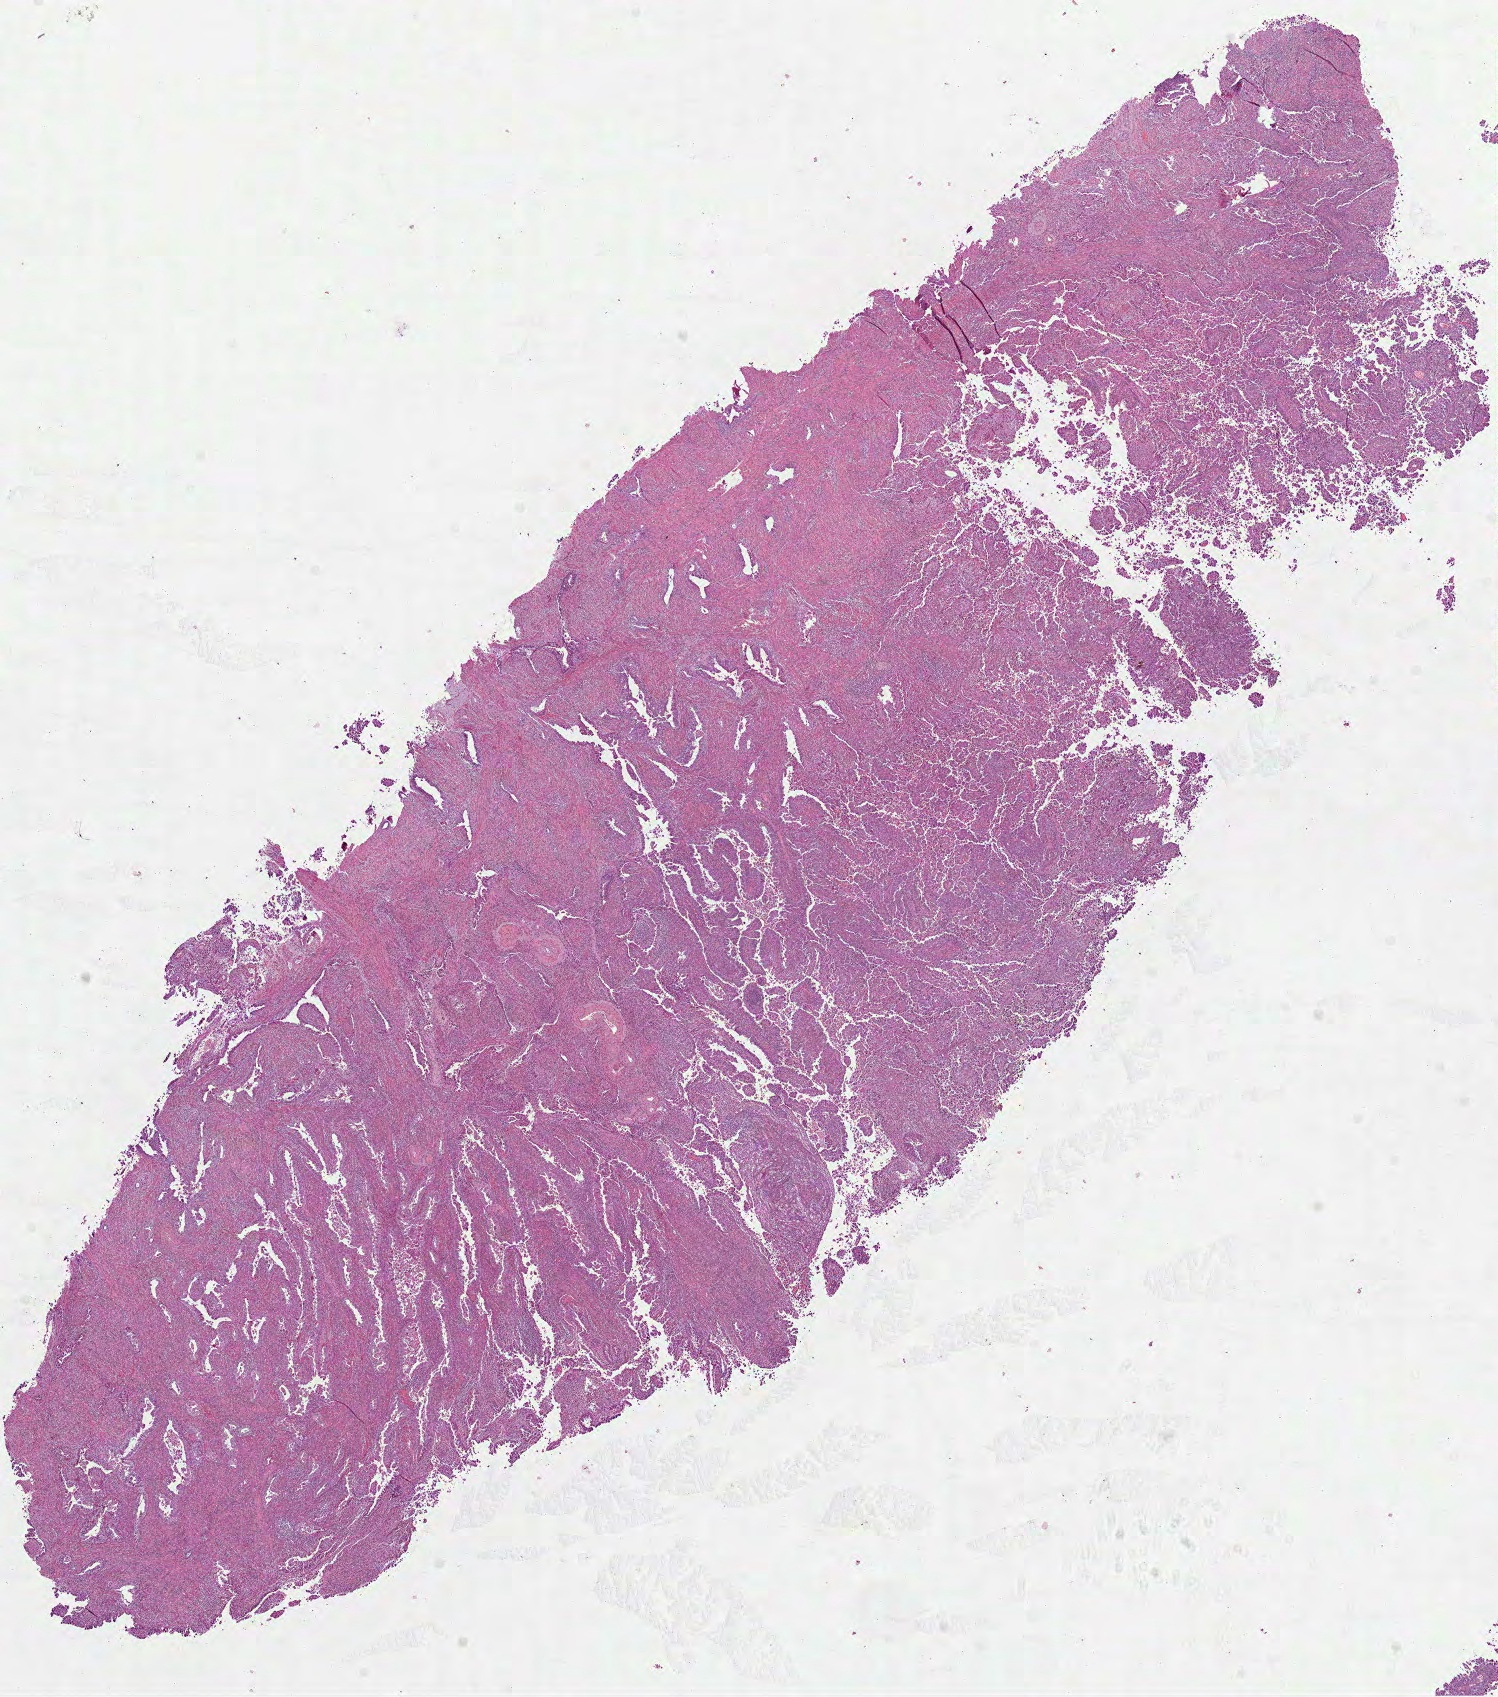
Whole-slide histology image, H&E — a low-resolution overview of the entire scanned area, about 12.1 x 13.7 mm. Formalin-fixed paraffin-embedded (FFPE) diagnostic section. Uterus, primary tumour sample. Patient: female, age at initial diagnosis 57 years. Histologic grade: G3 (poorly differentiated).
Histologic diagnosis: Papillary serous cystadenocarcinoma (endometrium). FIGO stage: IIIC2.